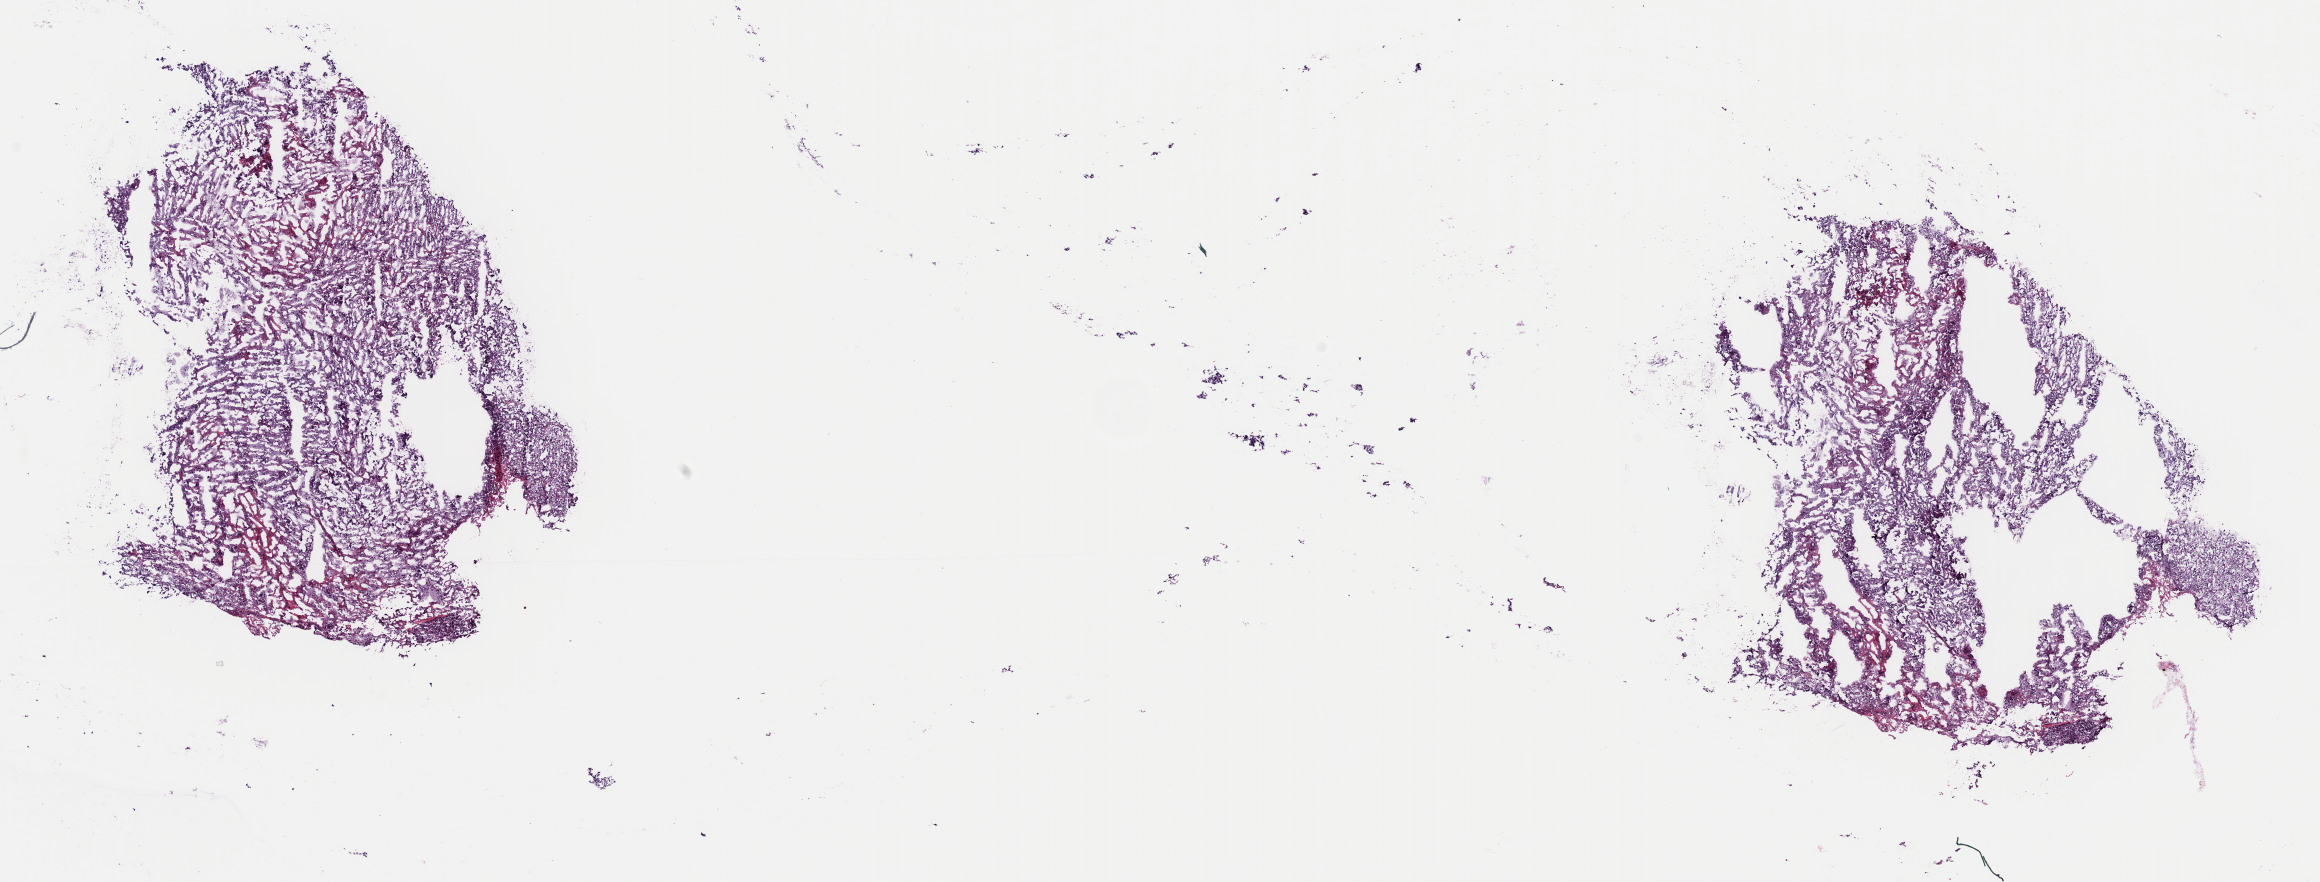
Whole-slide histology image, H&E — whole scanned area (about 18.3 x 7.0 mm) shown as a low-resolution overview; frozen section from the top of the tissue portion; adrenal gland, primary tumour sample. Patient: female, age at initial diagnosis 46 years. Pathologist review of this section (percent, as recorded): tumour cells 95%, tumour nuclei 80%, normal cells 0%, stromal cells 0%, necrosis 5%. Infiltration values recorded for this section: lymphocyte infiltration 1%, monocyte infiltration 0%, neutrophil infiltration 0%.
* diagnosis: Pheochromocytoma, NOS
* laterality: left